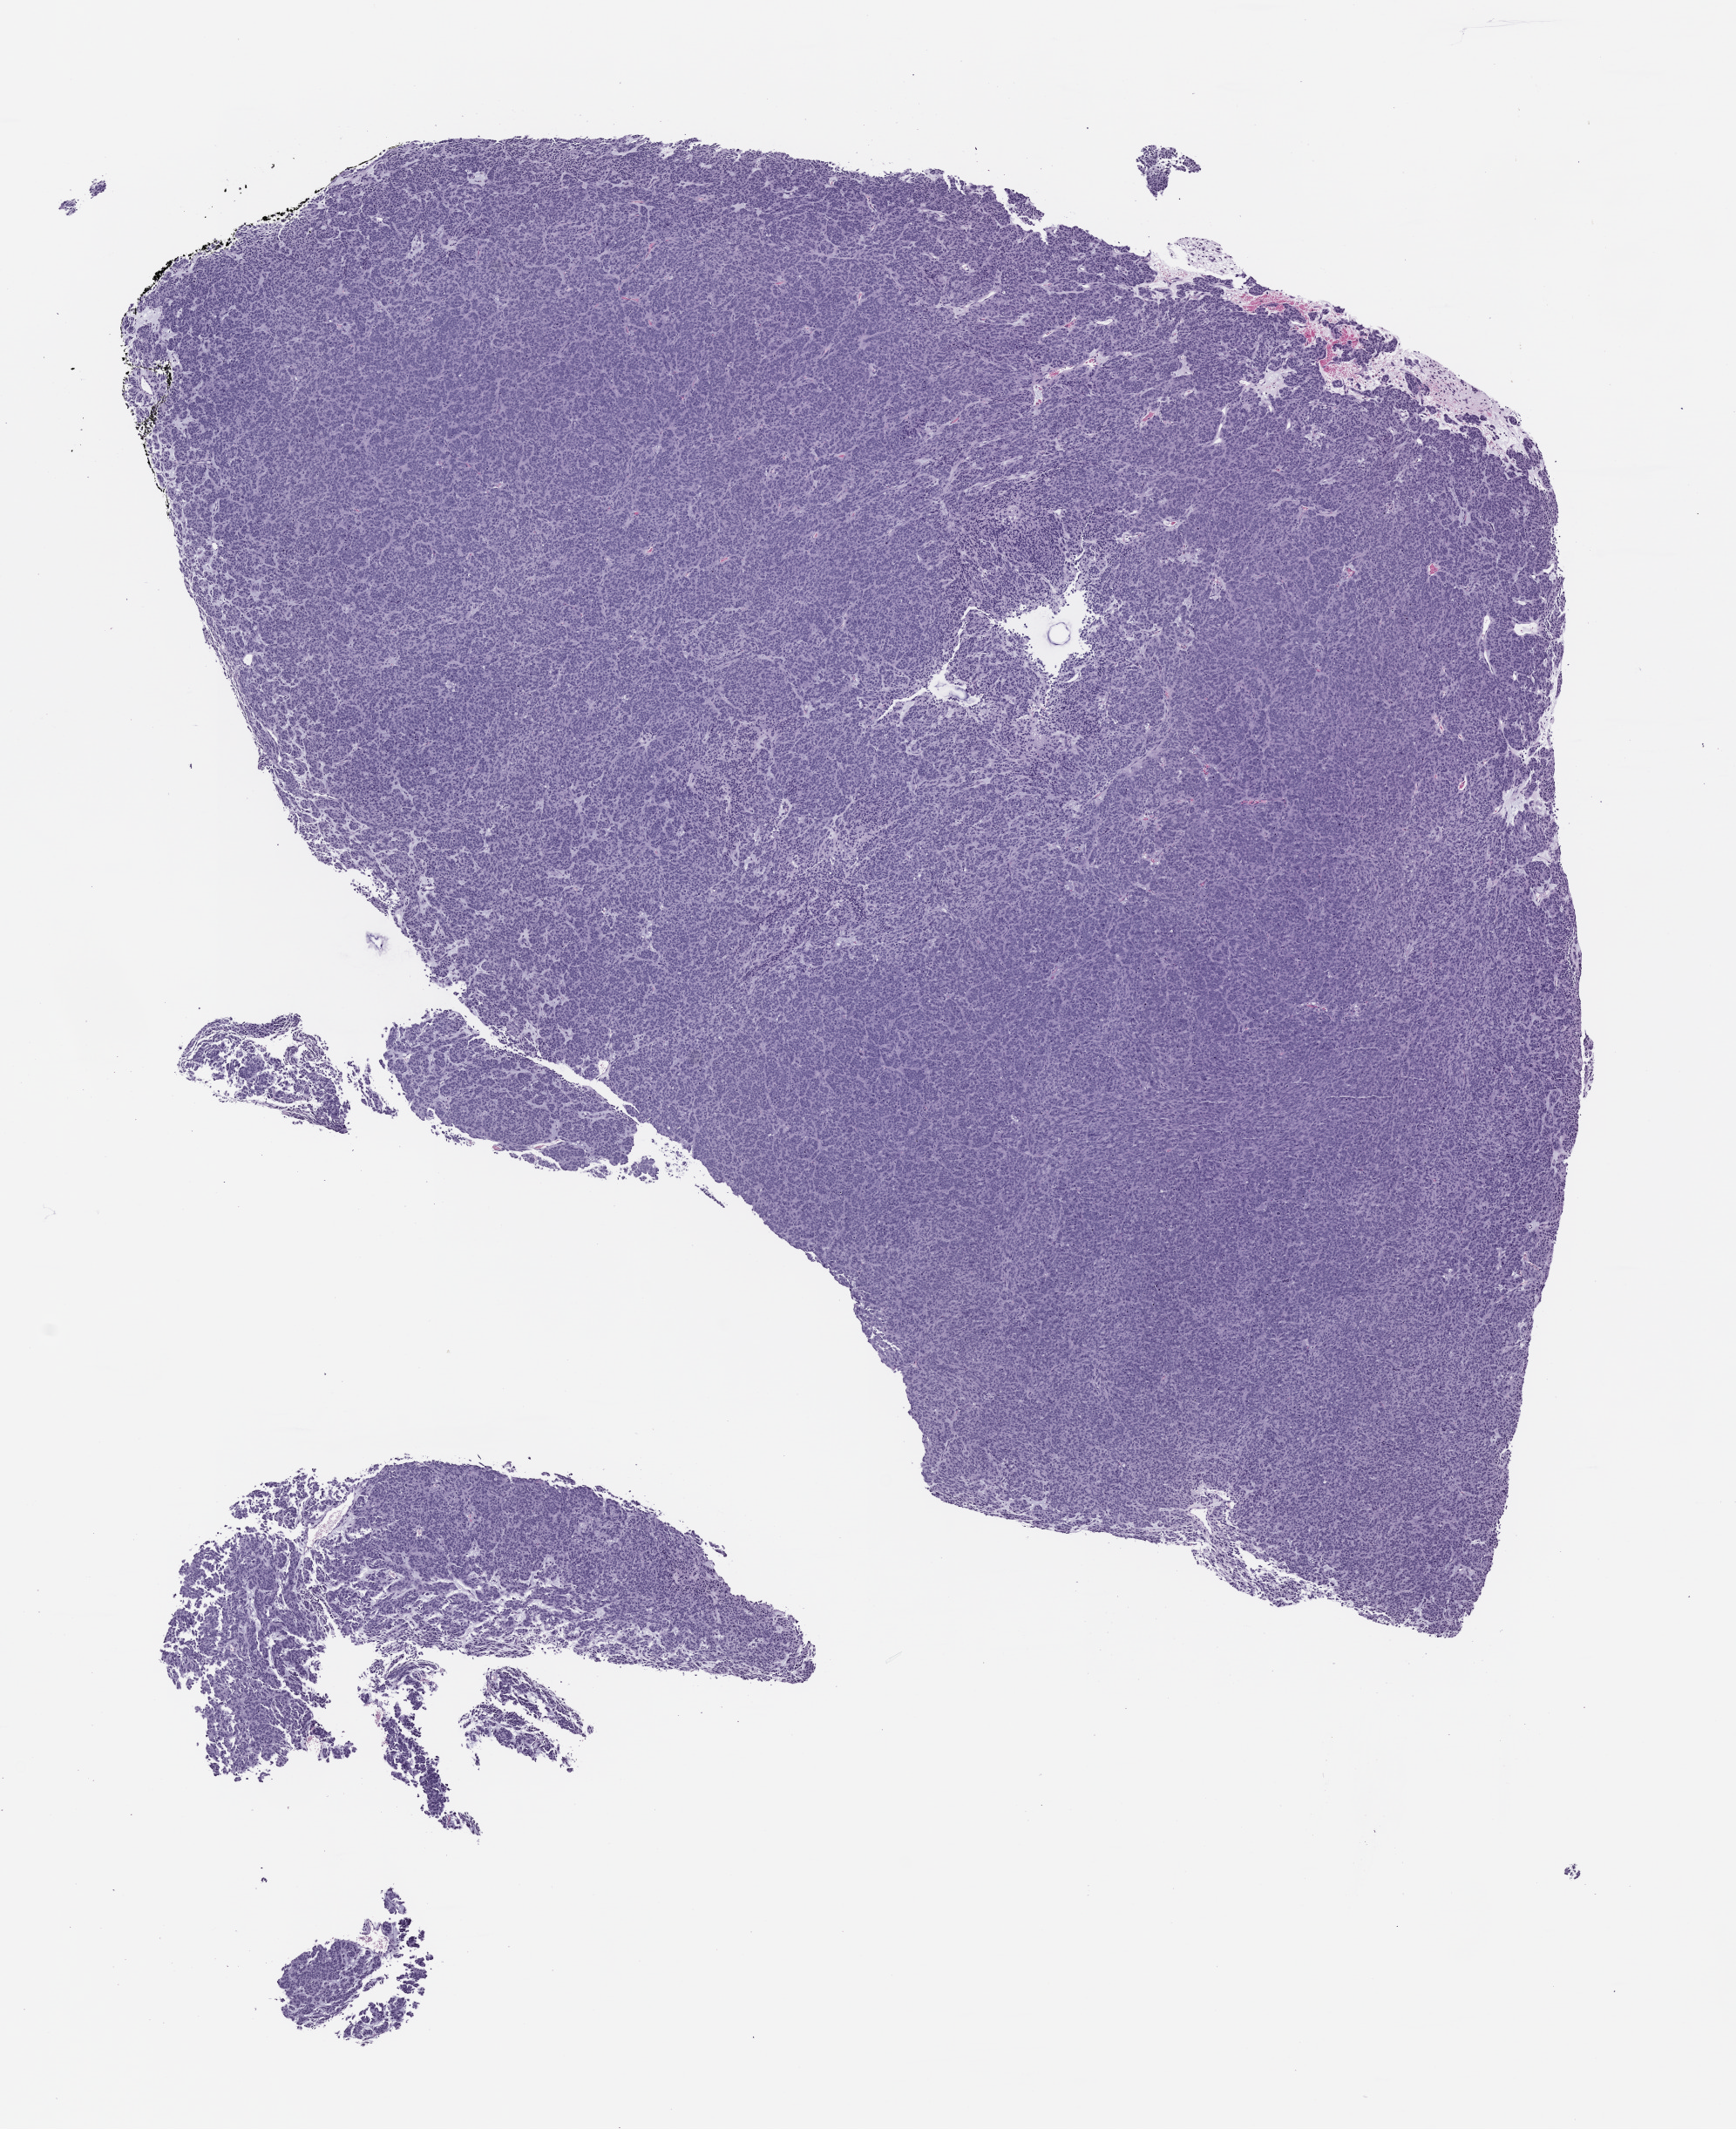
Haematoxylin and eosin whole-slide image of a patient-derived xenograft (PDX) tumor grown in a mouse, passage 1, shown as a low-resolution overview of the whole scanned area (about 8.0 x 9.8 mm), formalin-fixed, paraffin-embedded (FFPE) tissue, tumor site category: gastrointestinal tract.
Originating patient diagnosis: Gastrointestinal Stromal Tumor.